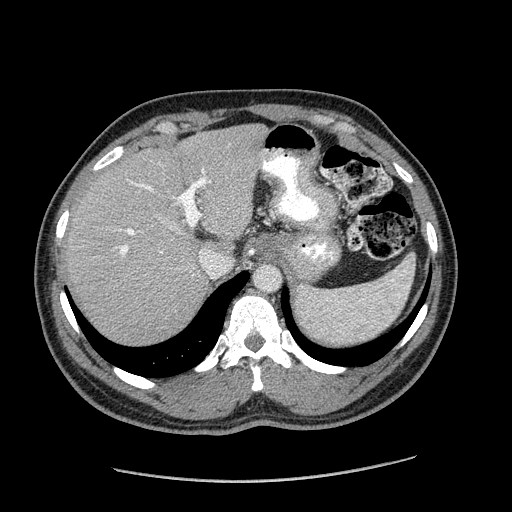
Contrast-enhanced abdominal CT (liver protocol), one axial slice; reconstruction kernel STANDARD; 120 kVp; soft-tissue window (W 400 / L 40 HU); 2.5 mm slice thickness; 512 × 512 image matrix, field of view 400 × 400 mm. Case-level facts recorded for this patient, not image findings: diagnosis: hepatocellular carcinoma (patient treated with transarterial chemoembolisation; whether this scan precedes or follows treatment is not stated here); TNM stage (as recorded): Stage-I; Child-Pugh class: A; tumour differentiation: well differentiated.
Structures marked on this image (semi-automatic segmentation, software-assisted and operator-edited):
- liver parenchyma outside the tumour (the mass and vessels are separate outlines, so this box may not span the whole liver): box from (x=64, y=124) to (x=266, y=344) px
- liver vessels: (x=119, y=170)–(x=210, y=275)